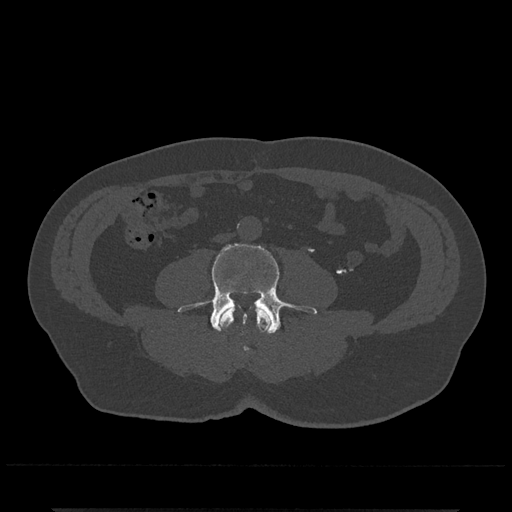
CT including the spine, one axial slice; slice 172 of 797 in the series (ordered by position); reconstruction kernel Br40s/3; bone window (W 1800 / L 400 HU); 0.5 mm slice thickness; 512 × 512 image matrix, field of view 393 × 393 mm. Patient: male, 67 years. Case-level facts recorded for this patient, not image findings: primary cancer: prostate.
Structures marked on this image (semi-automatically segmented with operator editing):
- L3 vertebra: bounding box (x1, y1, x2, y2) in pixels: (218, 306, 272, 351)
- L4 vertebra: (178, 243, 317, 334)